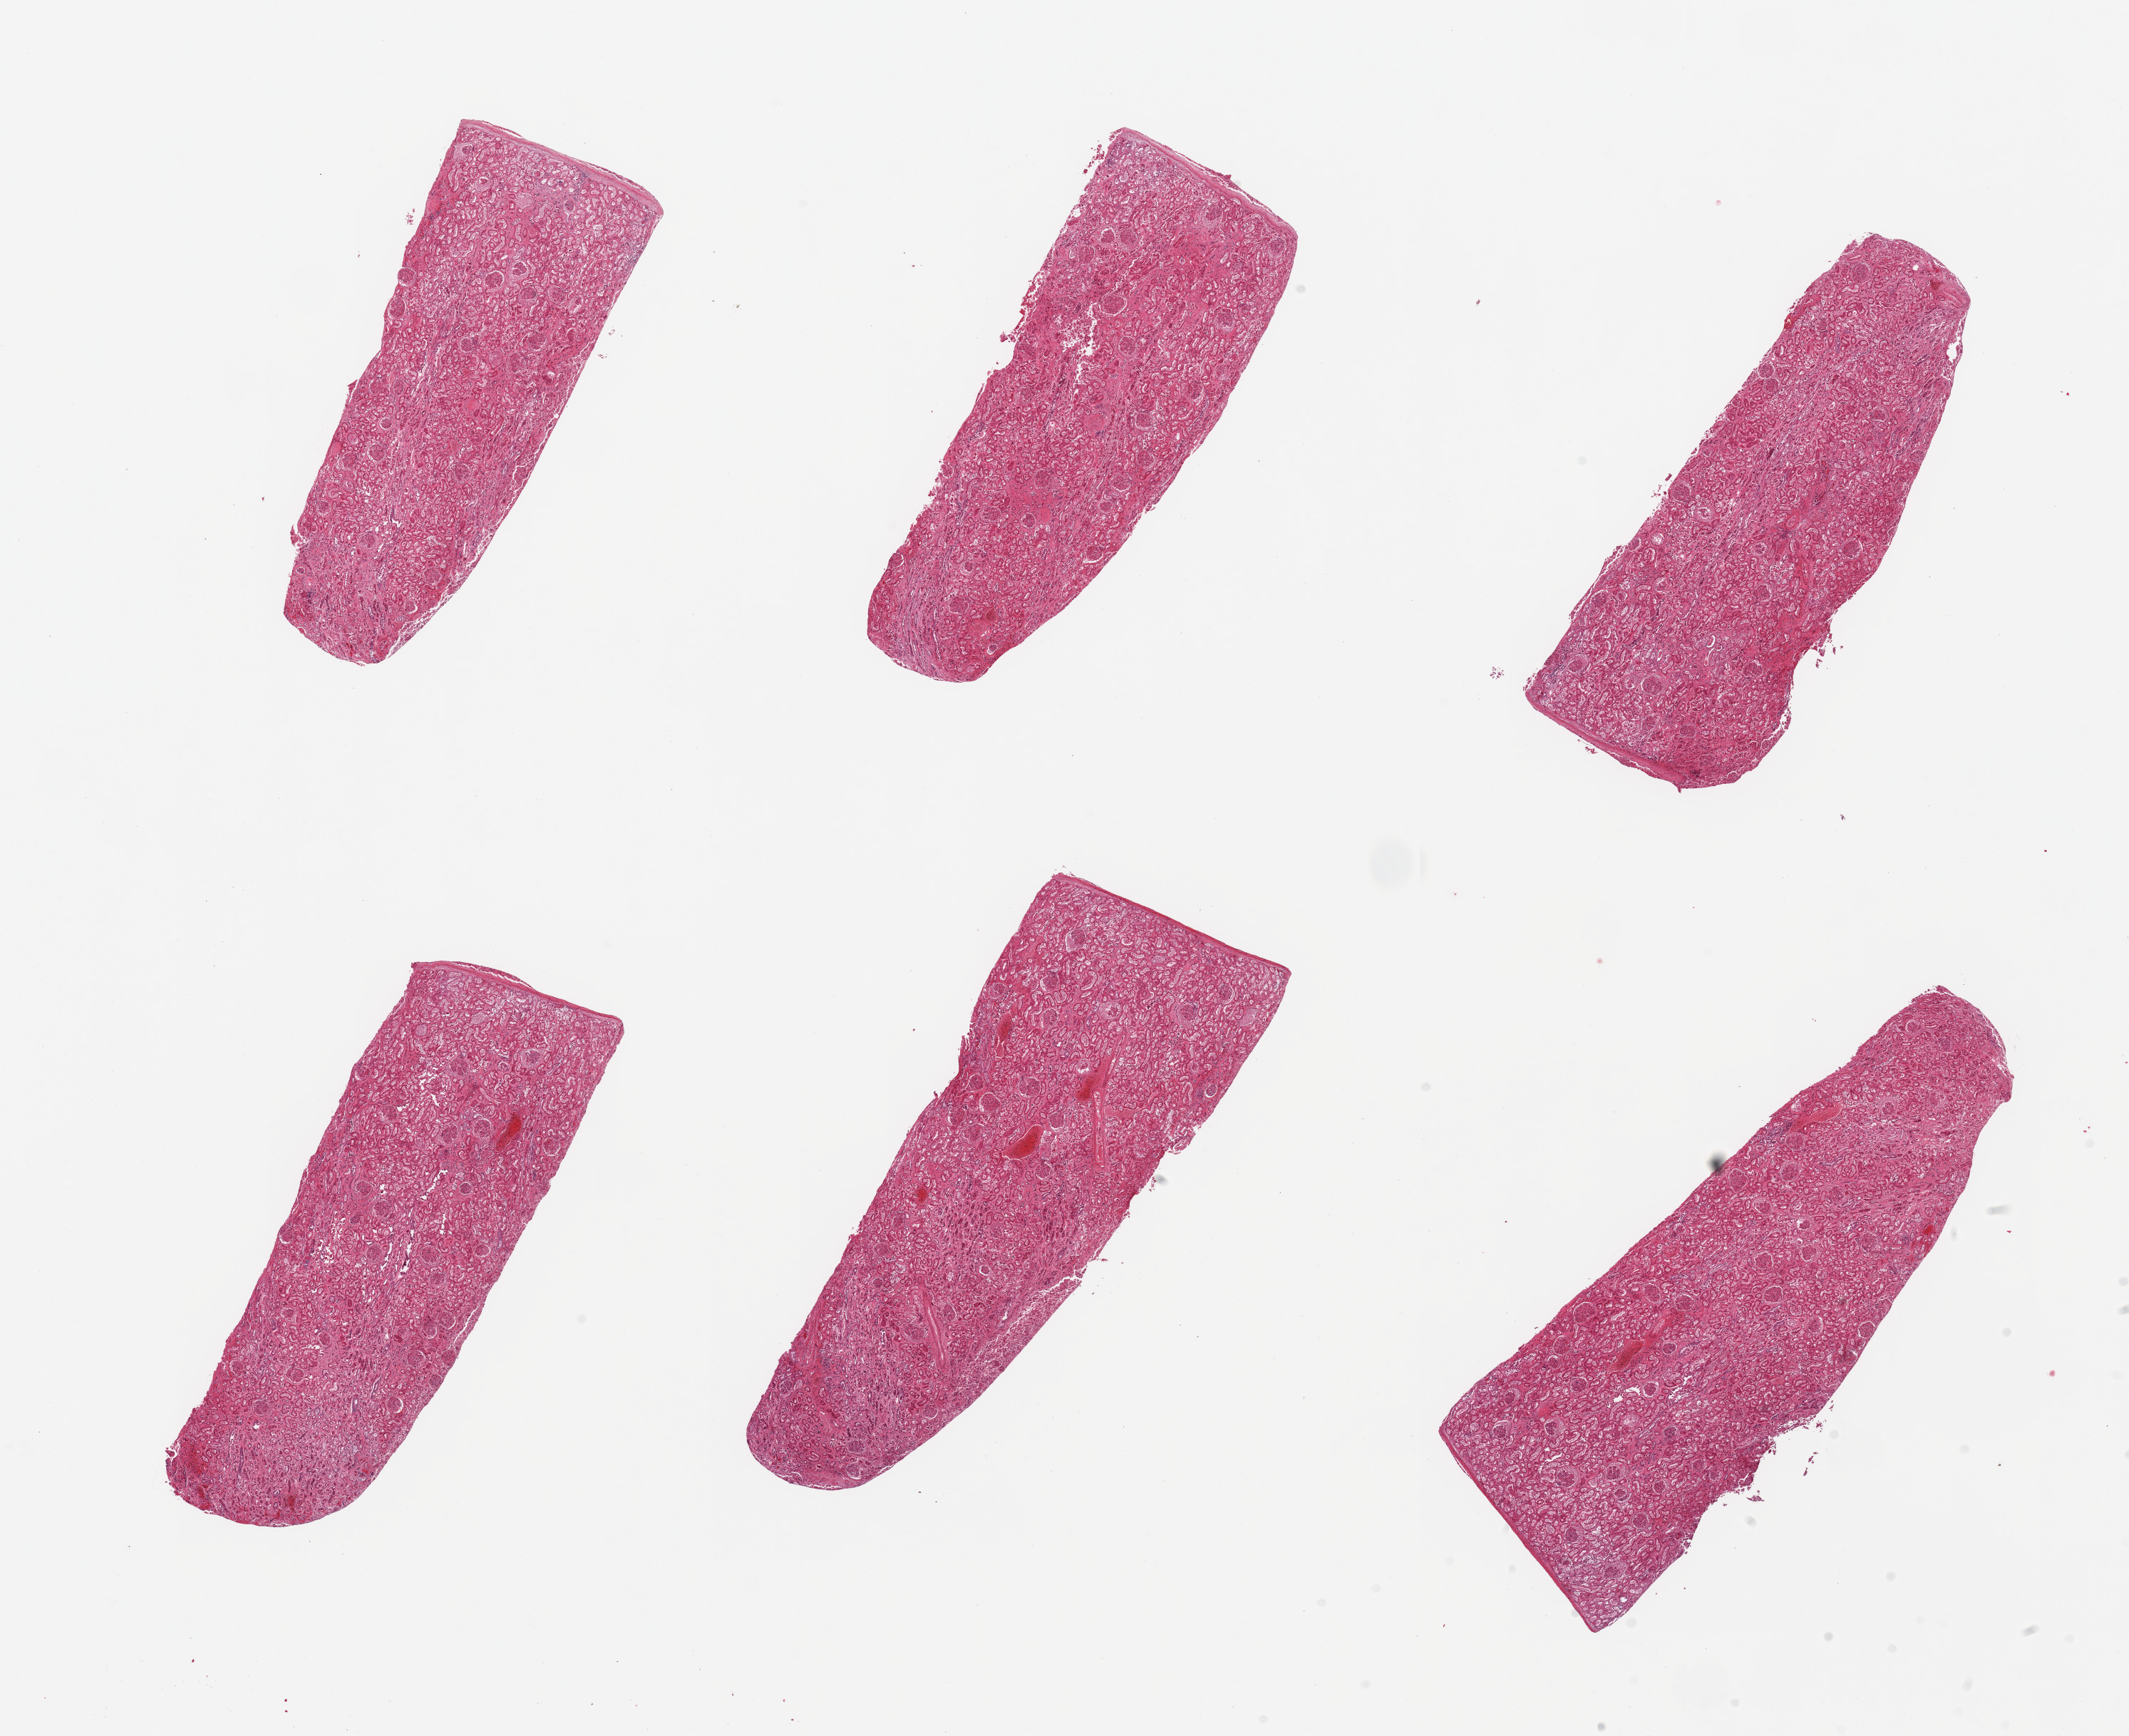
Digitized hematoxylin and eosin (H&E)-stained section — whole scanned area (about 23.6 x 19.3 mm, acquisition: 20x scan) shown as a low-resolution overview. PAXgene-fixed, paraffin-embedded tissue. Section of renal cortex (target tissue). Tissue donor sample. Donor: male.
Pathologist's review note for this sample: 6 pieces; glomeruli in all sections, few sclerotic, moderate to severe autolysis.